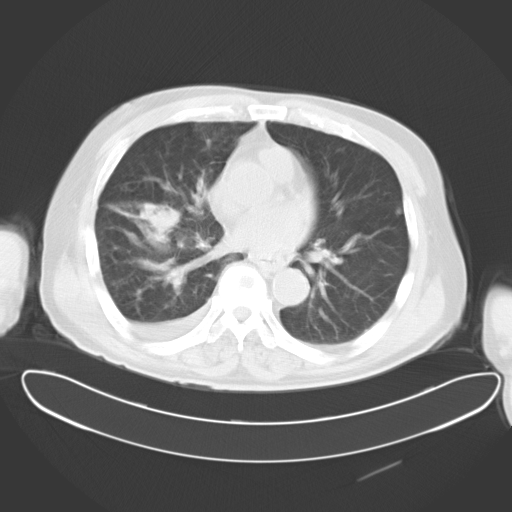
Chest CT, one axial slice. 120 kVp. Lung window (W 1500 / L -600 HU). 10 mm slice thickness. 512 × 512 image matrix, field of view 427 × 427 mm. Male patient, age 78 years. From the clinical record (not read from this slice): clinical TNM (as recorded): T2 N1 M1.
Outlined on this slice (bounding box drawn by a radiologist):
- lung tumour (recorded histology: adenocarcinoma): box from (x=129, y=193) to (x=187, y=238) px